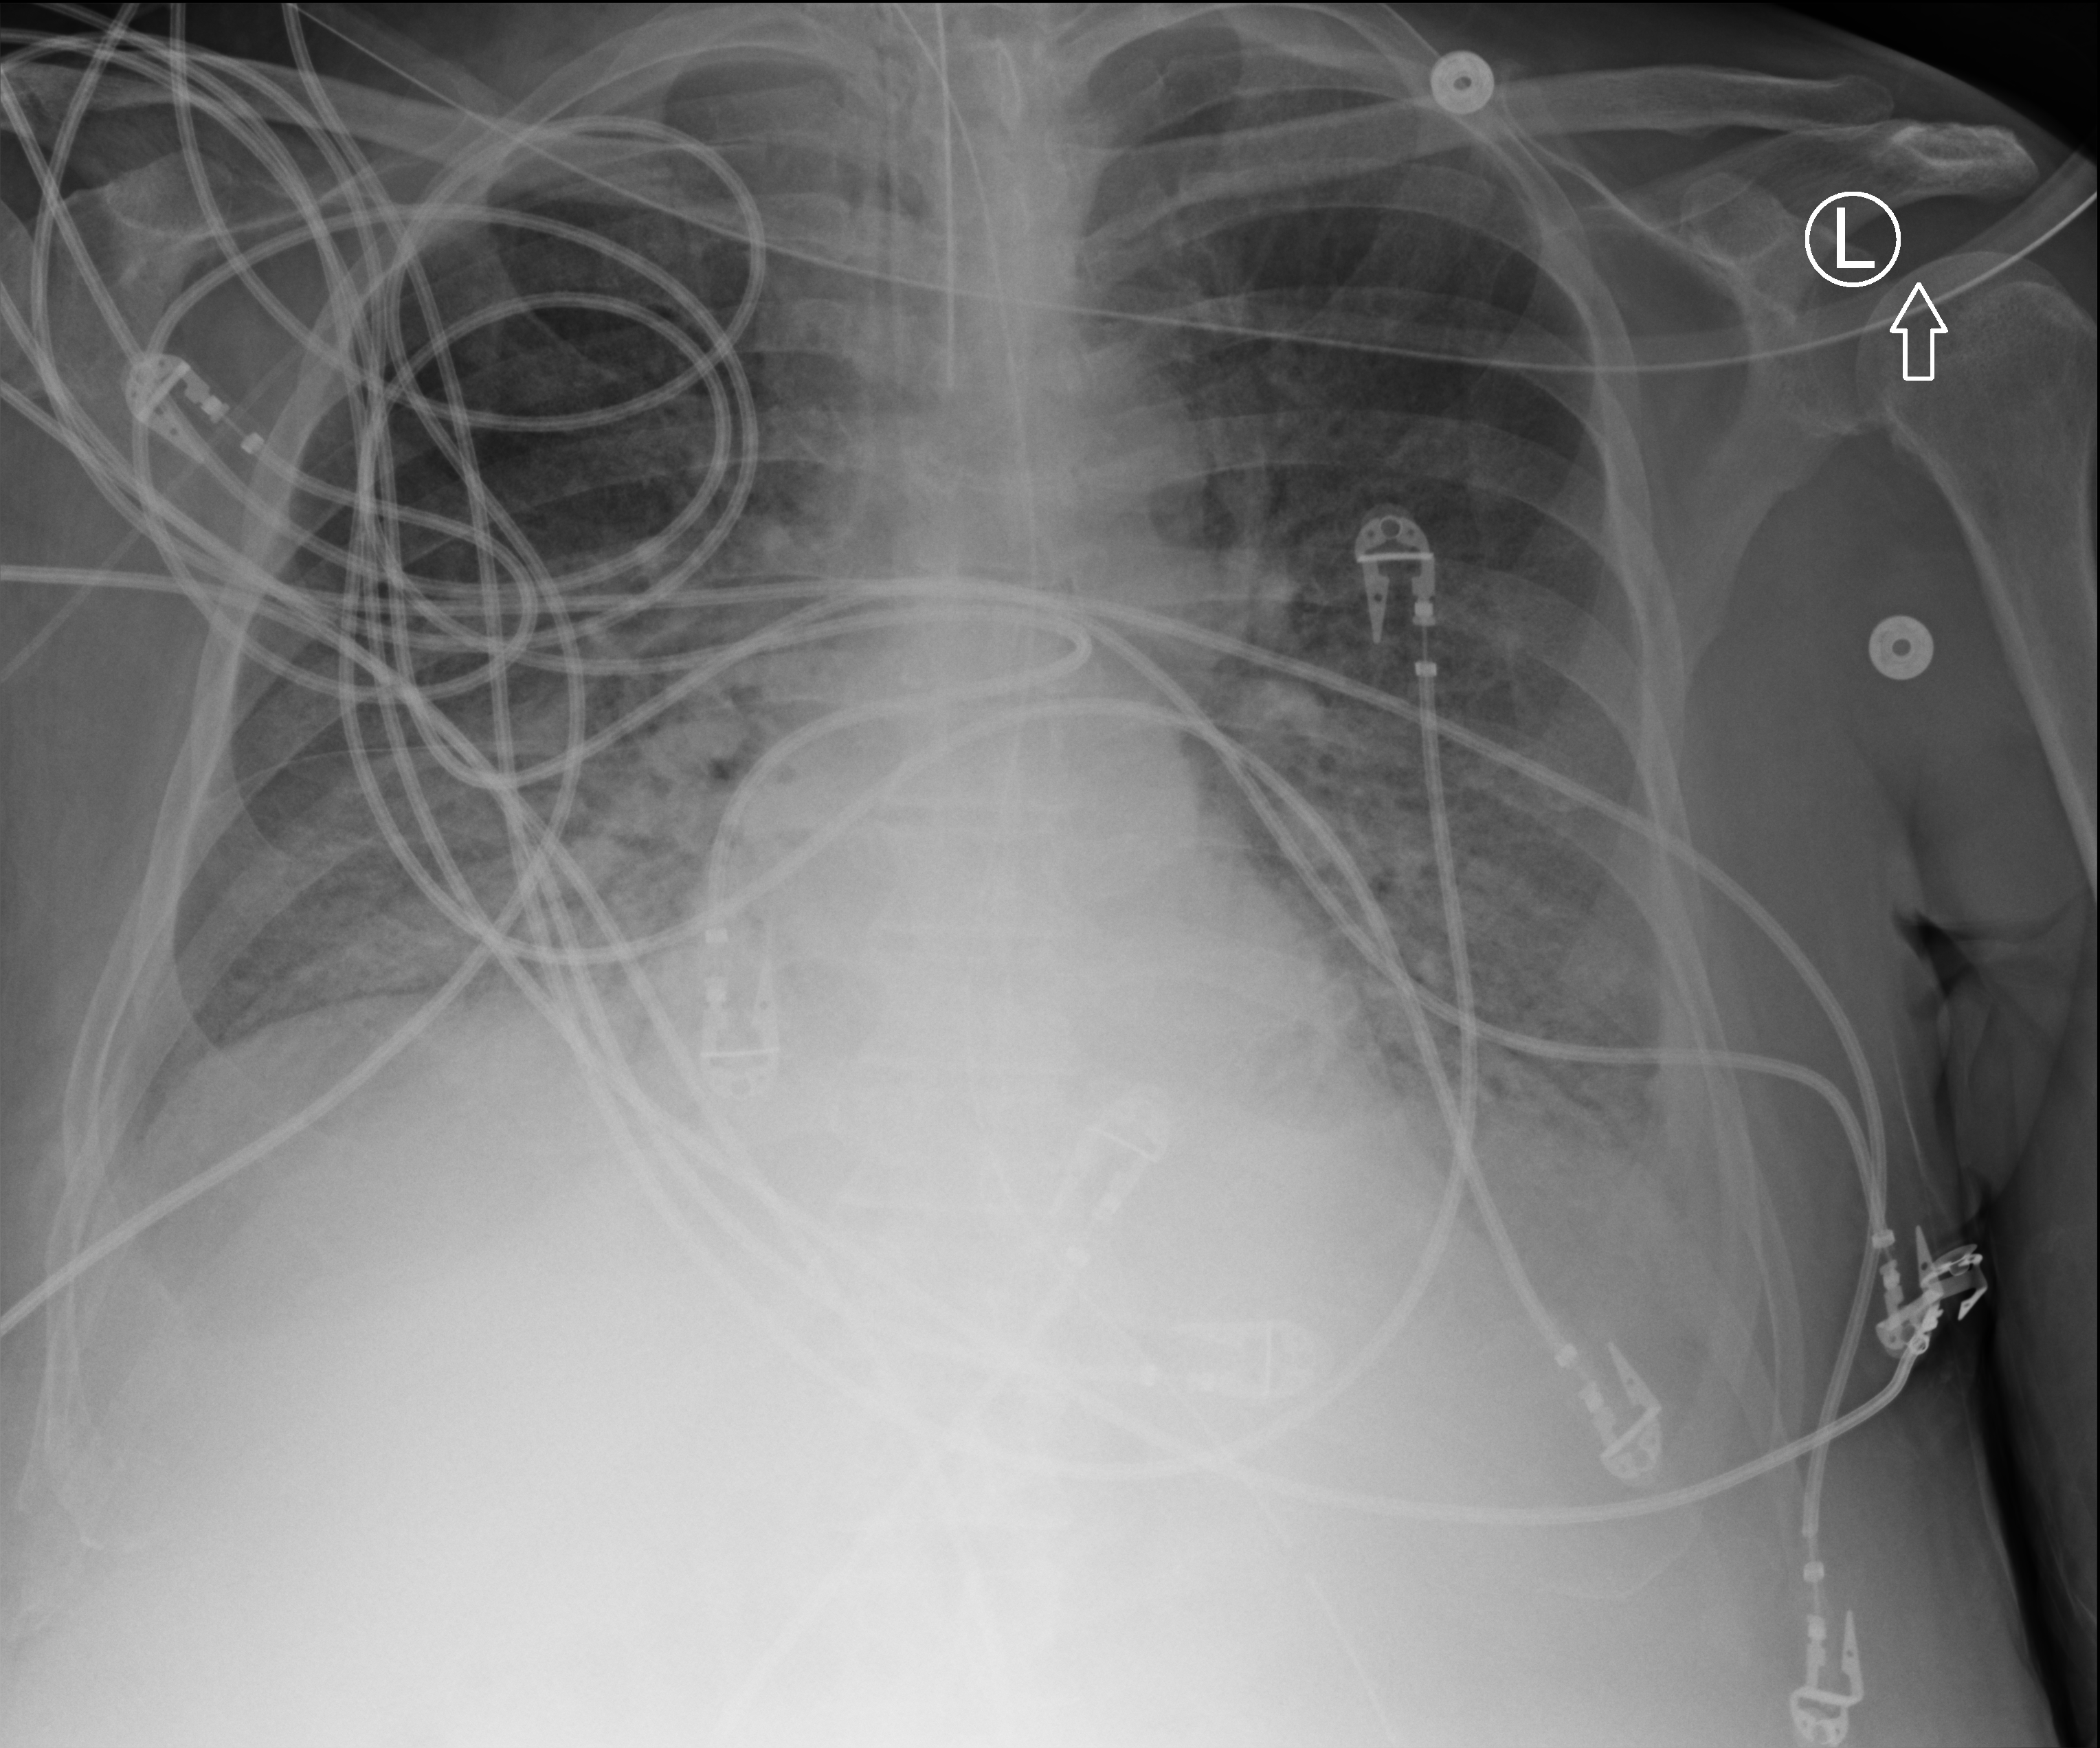
Bedside chest radiograph (computed radiography); anteroposterior (AP) projection. Patient hospitalised with COVID-19; male, aged 60–74 years.
From the hospital-stay record, not from the radiograph (when in the stay this image was taken is not recorded): mechanically ventilated during this hospital stay: yes; admitted to intensive care during this hospital stay: yes.